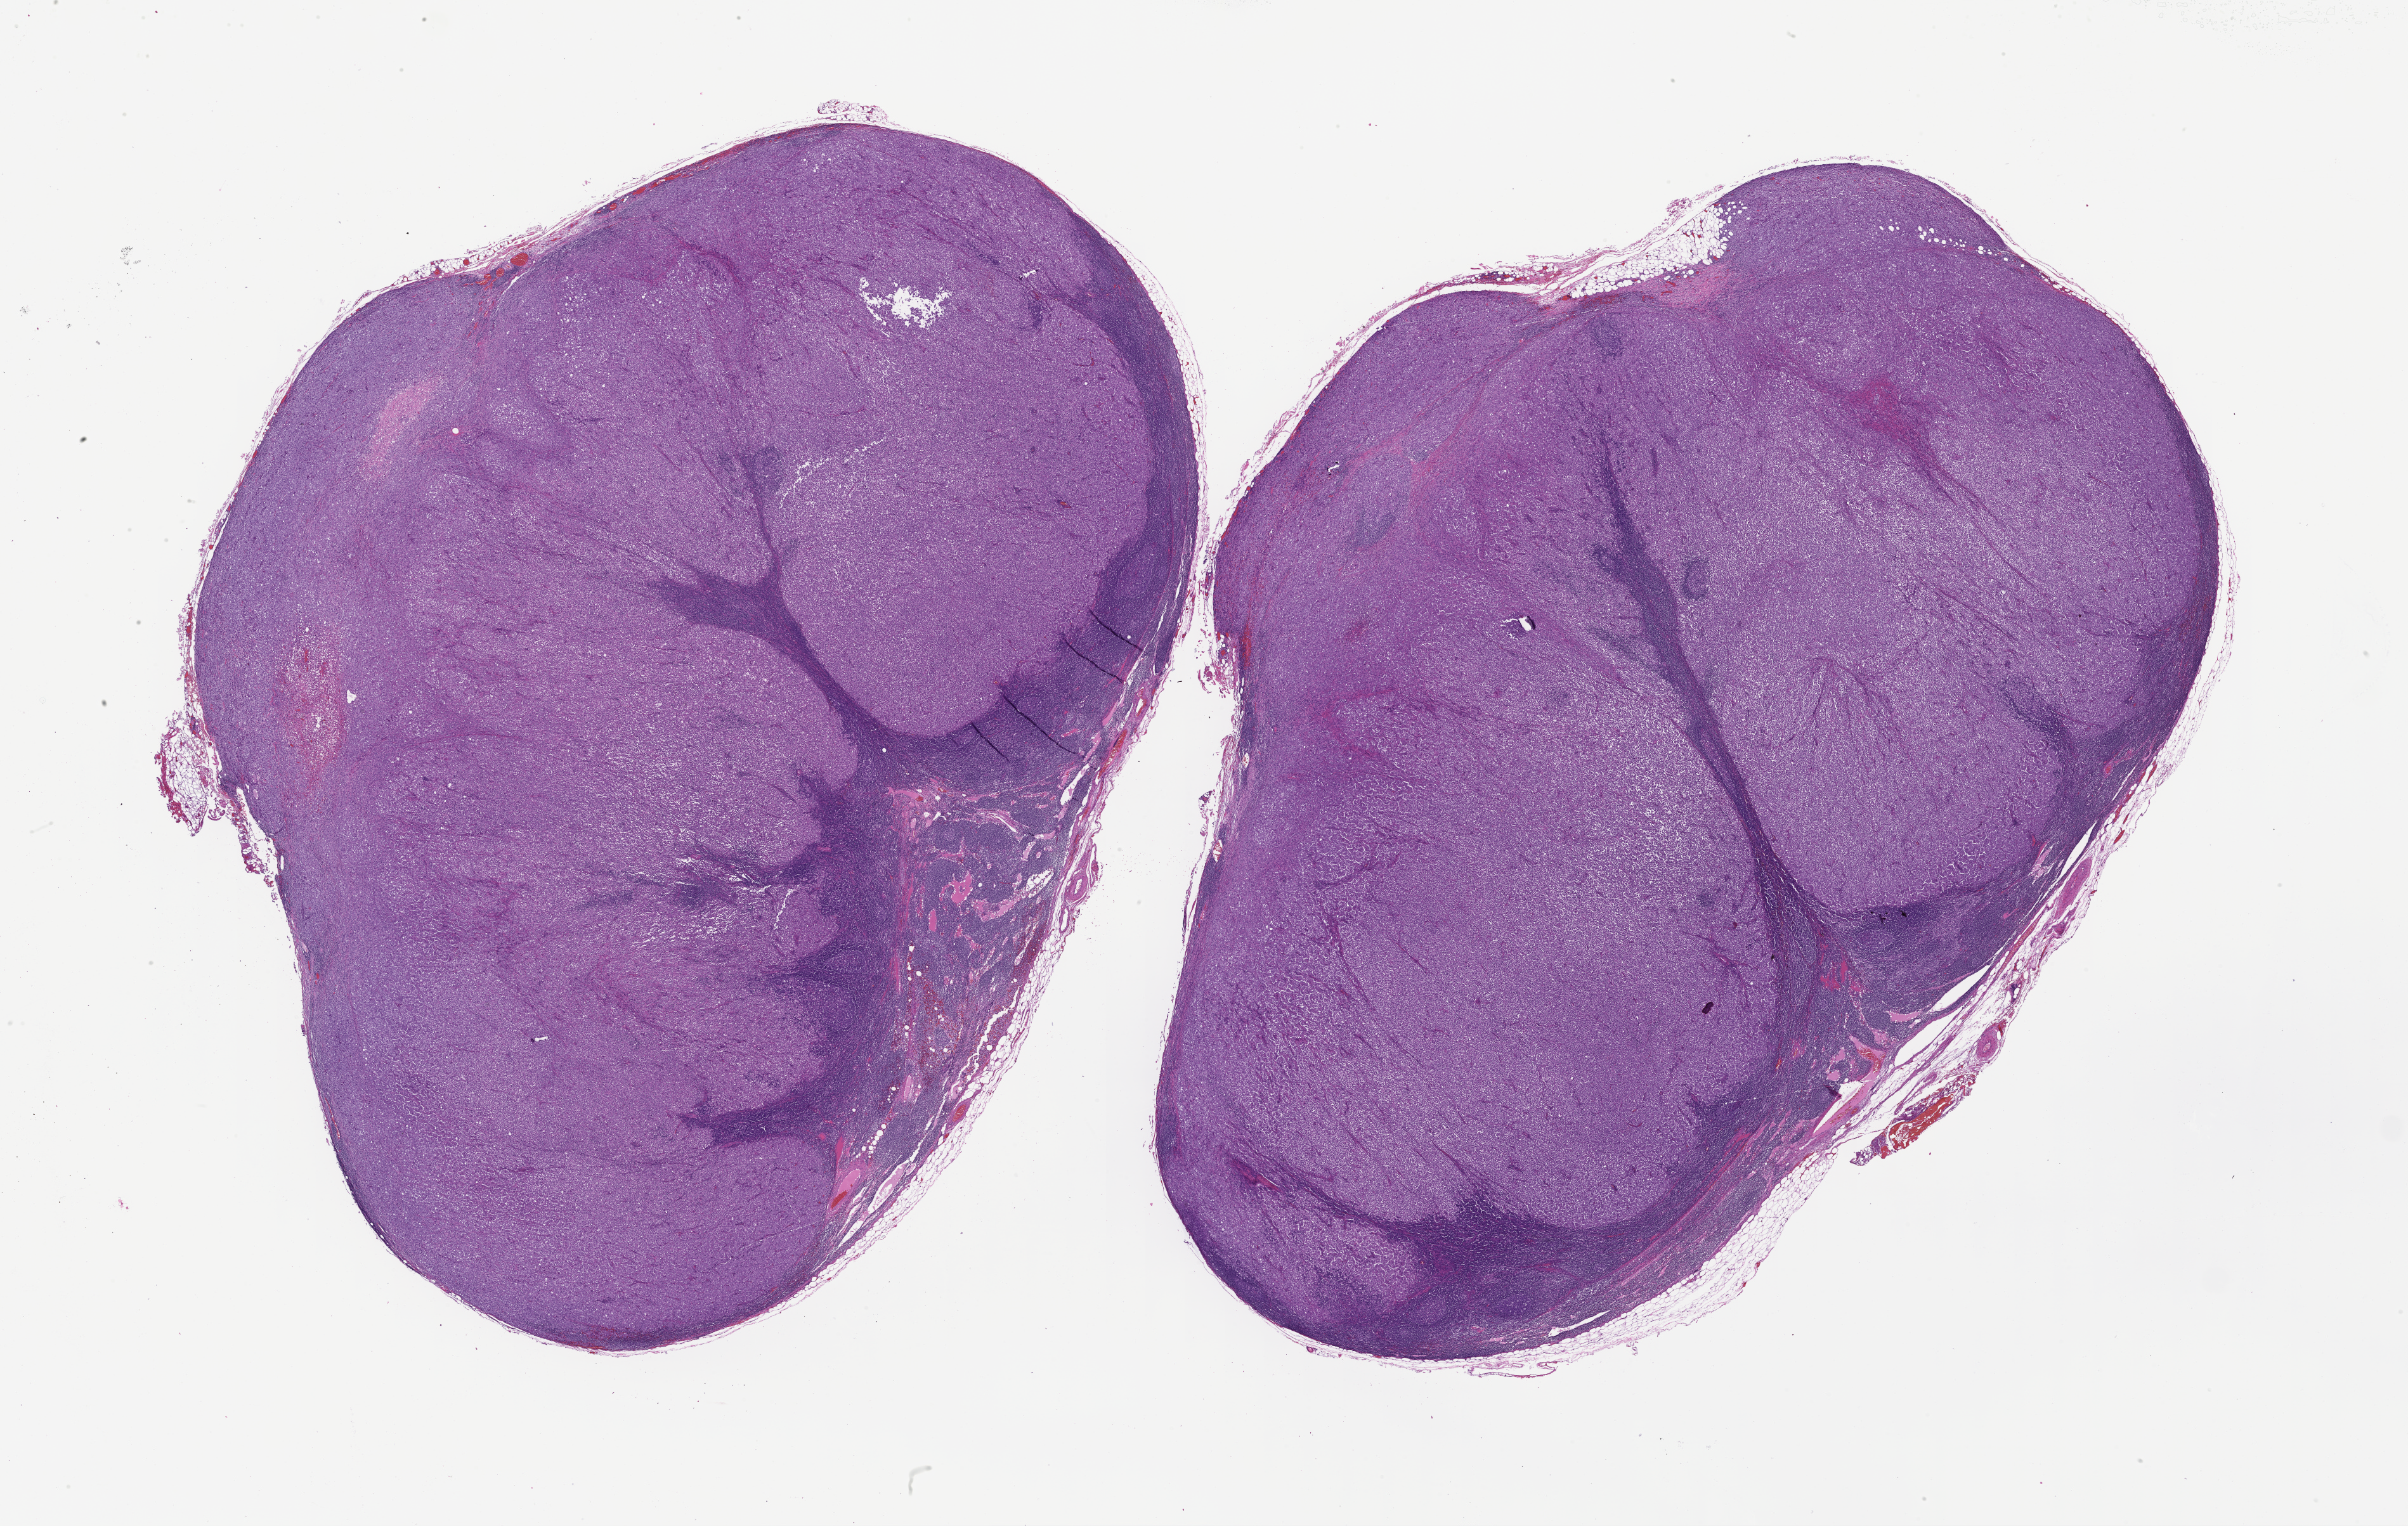
Whole-slide image, H&E stain, whole scanned area (about 30.7 x 19.4 mm) shown as a low-resolution overview, formalin-fixed paraffin-embedded section, archival tissue. Patient sex: male.
This section: metastasis (sampled organ not recorded). Primary diagnosis of the patient: Melanoma.